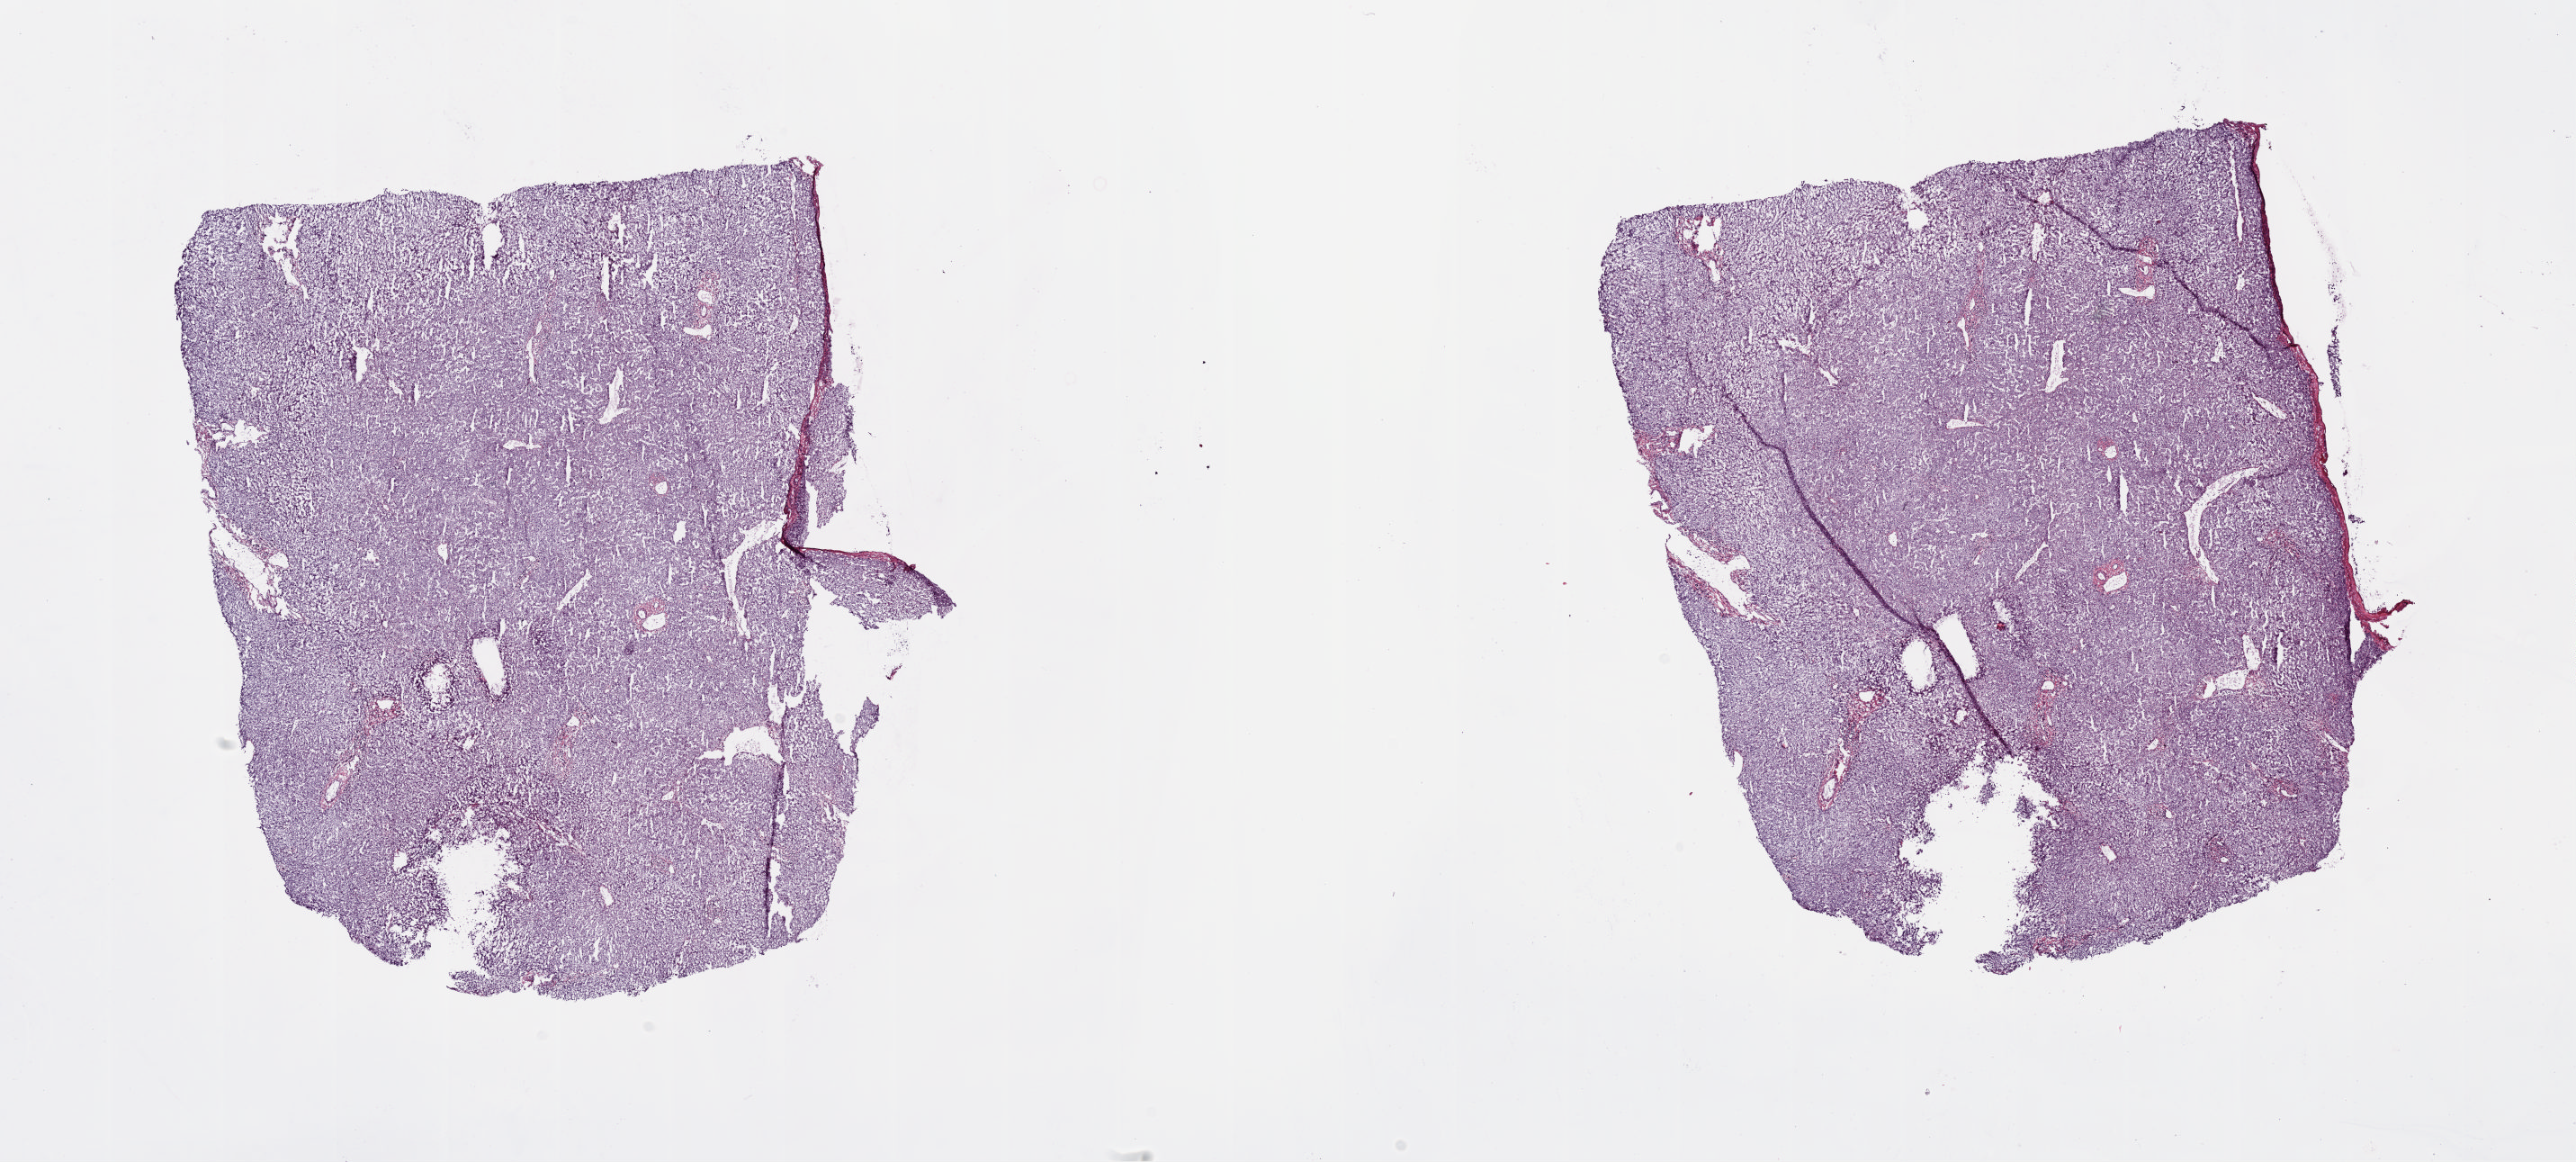
Digitized H&E tissue section (whole slide) — shown as a low-resolution overview of the whole scanned area (about 22.6 x 10.2 mm). Frozen section from the top of the tissue portion. Liver, solid tissue normal (non-tumour tissue) sample. Female, age 80 years at initial diagnosis. Slide review estimates, as recorded: tumour cells 0%, tumour nuclei 0%, normal cells 100%, stromal cells 0%, necrosis 0%. Infiltration values recorded for this section: lymphocyte infiltration 2%, monocyte infiltration 6%, neutrophil infiltration 0%.
* this section: solid tissue normal (non-tumour) sample from the same patient
* patient diagnosis: Hepatocellular carcinoma, NOS